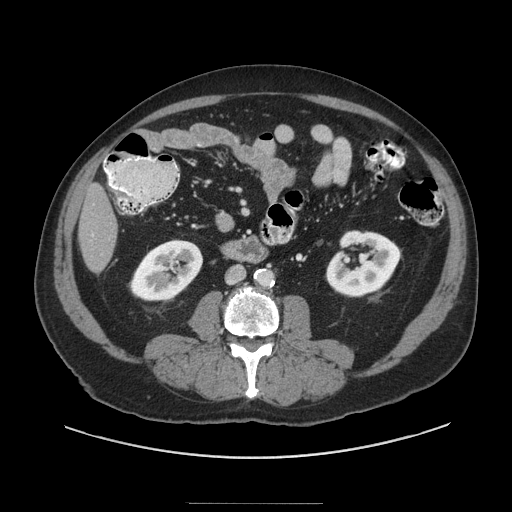
Contrast-enhanced abdominal CT (liver protocol), one axial slice; position 20 of 91 along the scan axis; reconstruction kernel STANDARD; 140 kVp; soft-tissue window (W 400 / L 40 HU); 2.5 mm slice thickness; 512 × 512 image matrix. Case-level facts recorded for this patient, not image findings: diagnosis: hepatocellular carcinoma (patient treated with transarterial chemoembolisation; whether this scan precedes or follows treatment is not stated here); TNM stage (as recorded): Stage-I; Child-Pugh class: A; tumour differentiation: well differentiated; tumour size: 4 cm.
Outlined on this slice (semi-automatically segmented with operator editing):
- liver parenchyma outside the tumour (the mass and vessels are separate outlines, so this box may not span the whole liver): box from (x=78, y=184) to (x=118, y=272) px